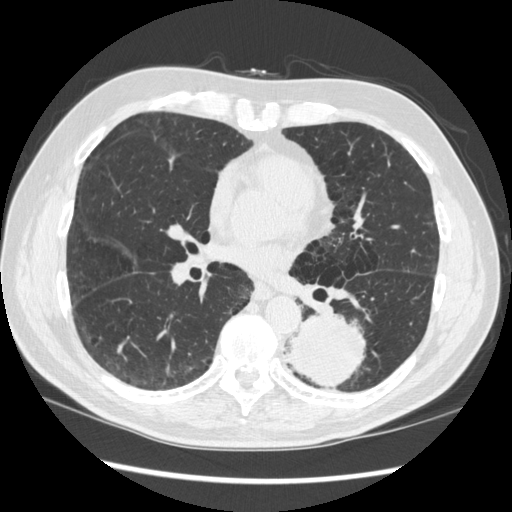
Low-dose screening chest CT, one axial slice. Slice 154 of 348 in the series (ordered by position). Reconstruction kernel STANDARD. 120 kVp. Lung window (W 1500 / L -600 HU). 1.25 mm slice thickness. 512 × 512 image matrix, field of view 360 × 360 mm.
Annotated regions visible in this slice (expert manual segmentation):
- lesion 1 (tumor, lower lobe of left lung): box from (x=286, y=314) to (x=365, y=390) px